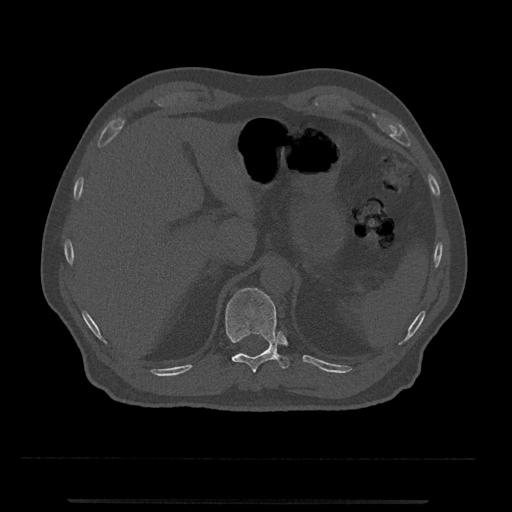
CT including the spine, one axial slice; 120 kVp; bone window (W 1800 / L 400 HU); 512 × 512 image matrix. Male patient, age 63 years. From the clinical record (not read from this slice): primary cancer: prostate.
Outlined on this slice (semi-automatic segmentation, software-assisted and operator-edited):
- T11 vertebra: bounding box <225,287,290,373> (left, top, right, bottom; pixels)